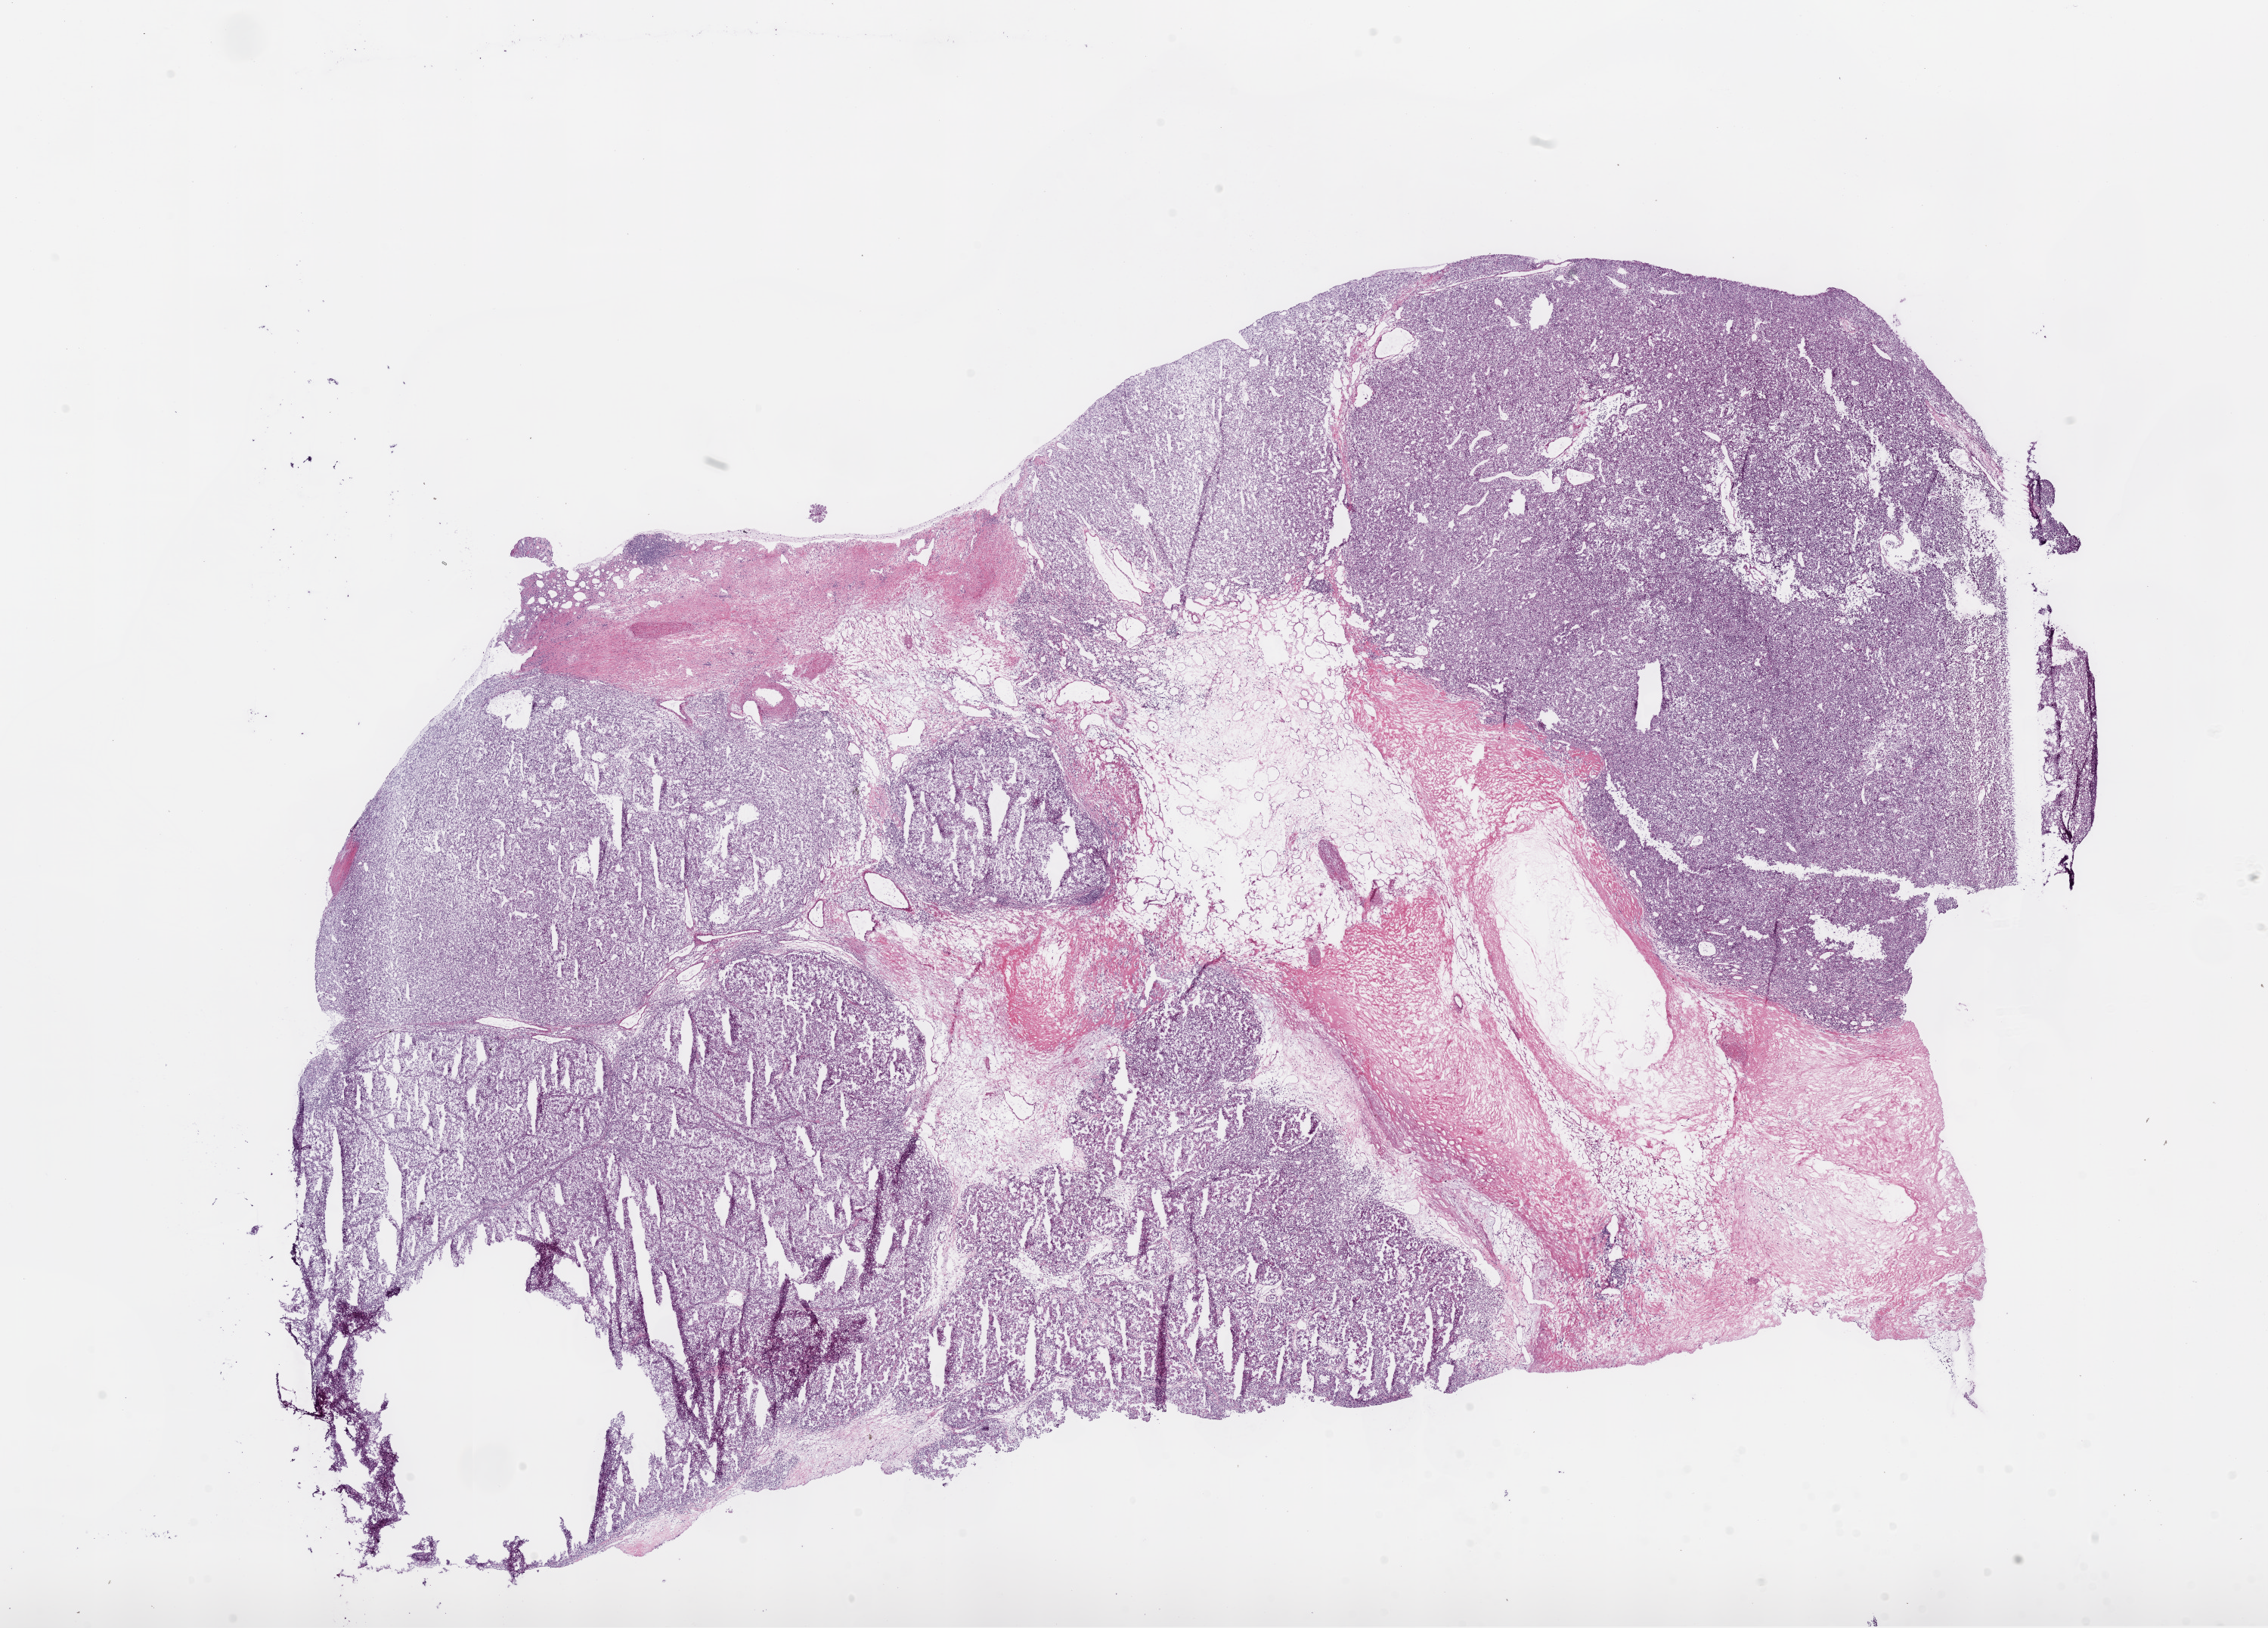
Digitized H&E tissue section (whole slide) — whole scanned area (about 24.1 x 17.3 mm, slide scanned at 20x) shown as a low-resolution overview, frozen section from the bottom of the tissue portion, primary tumour sample from the kidney. Male patient; age at initial diagnosis 57 years. Histologic grade: G3 (poorly differentiated). Pathologist review of this section (percent, as recorded): tumour cells 77%, tumour nuclei 85%, normal cells 3%, stromal cells 20%, necrosis 0%.
AJCC pathologic stage: III. Histologic diagnosis: Clear cell adenocarcinoma, NOS. Lymph nodes positive (case pathology): 0 of 21 examined.